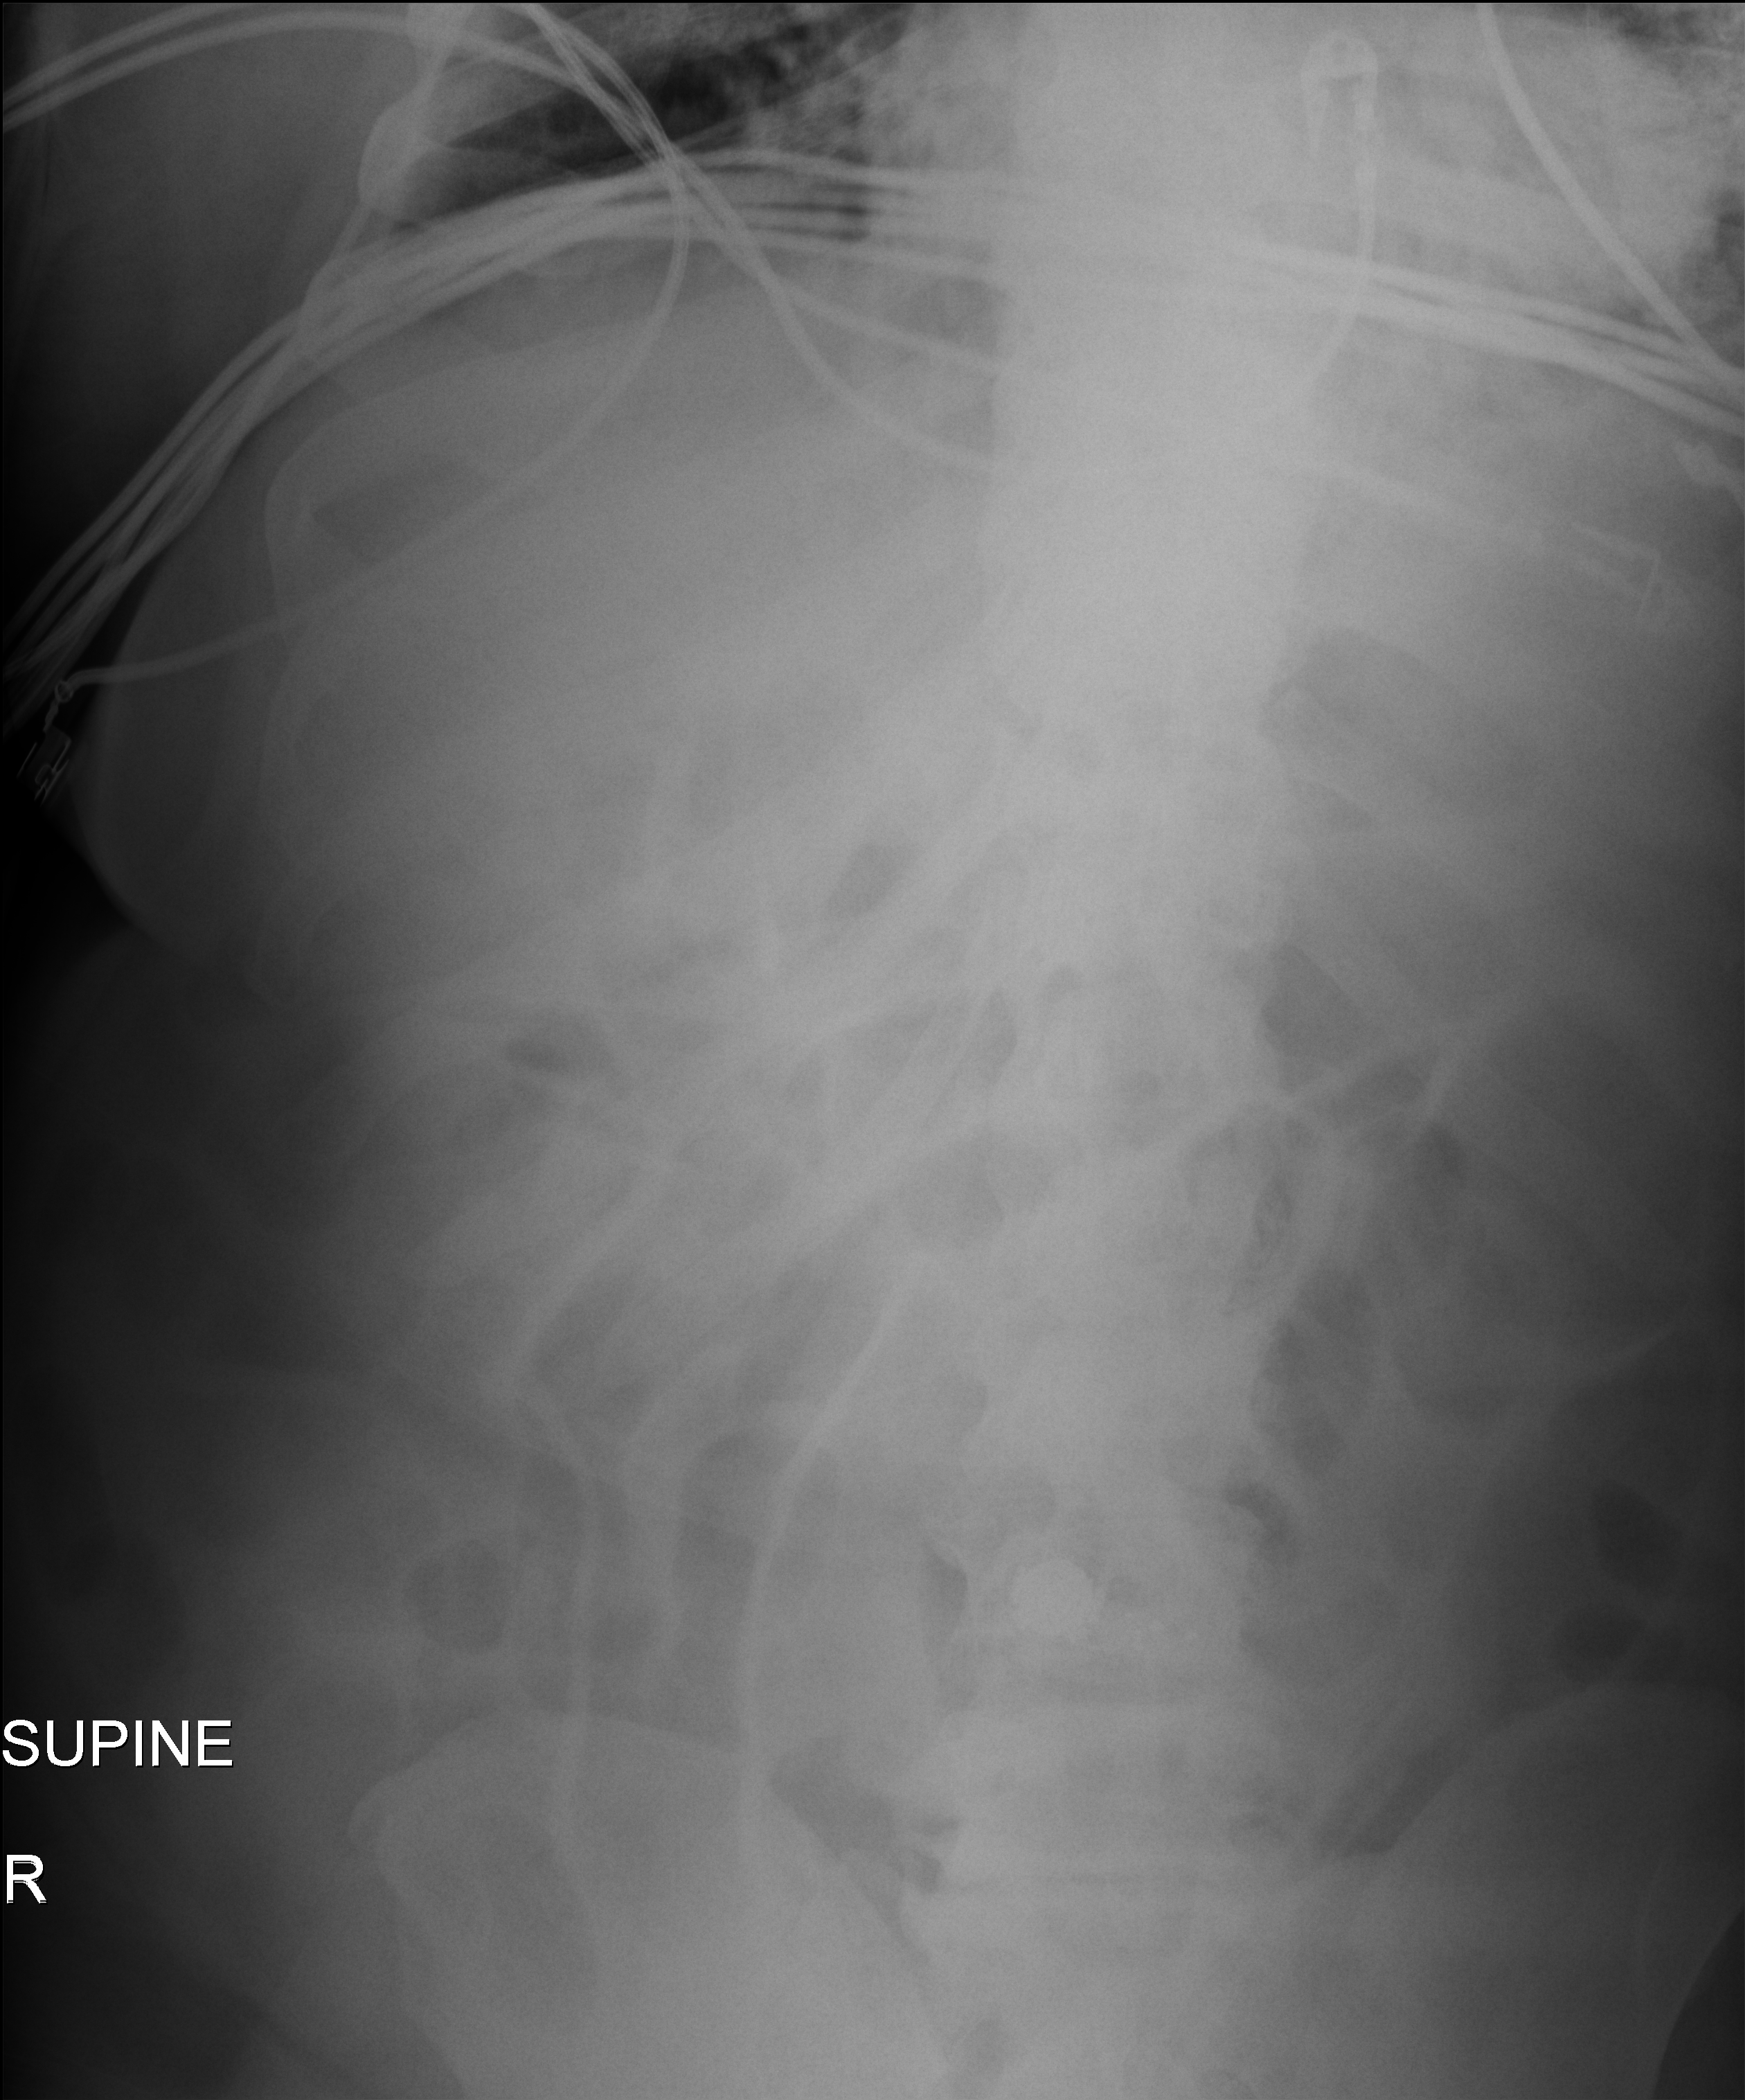
Portable abdomen radiograph, anteroposterior (AP) projection. Male patient hospitalised with COVID-19, age 18–59 years.
From the hospital-stay record, not from the radiograph (when in the stay this image was taken is not recorded):
- mechanically ventilated during this hospital stay: yes